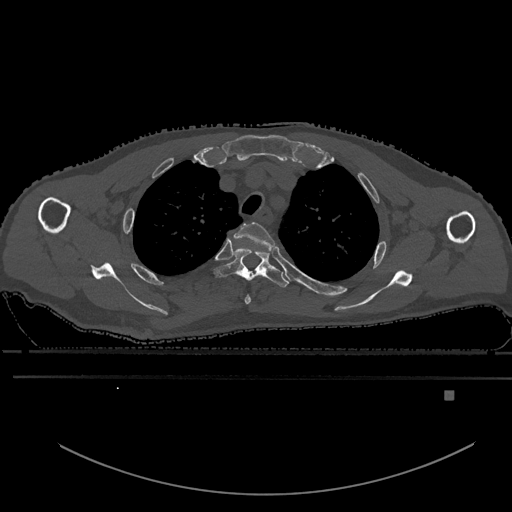
CT including the spine, one axial slice. Slice 465 of 969 in the series (ordered by position). Bone window (W 1800 / L 400 HU). 512 × 512 image matrix, field of view 456 × 456 mm. Patient: male, 82 years. Case-level facts recorded for this patient, not image findings: primary cancer: prostate; vertebrae with lytic lesions (as recorded): T11, T9, T8, T2.
Outlined on this slice (semi-automatically segmented with operator editing):
- T2 vertebra: bounding box <234,221,275,305> (left, top, right, bottom; pixels)
- T3 vertebra: <214,249,289,287>